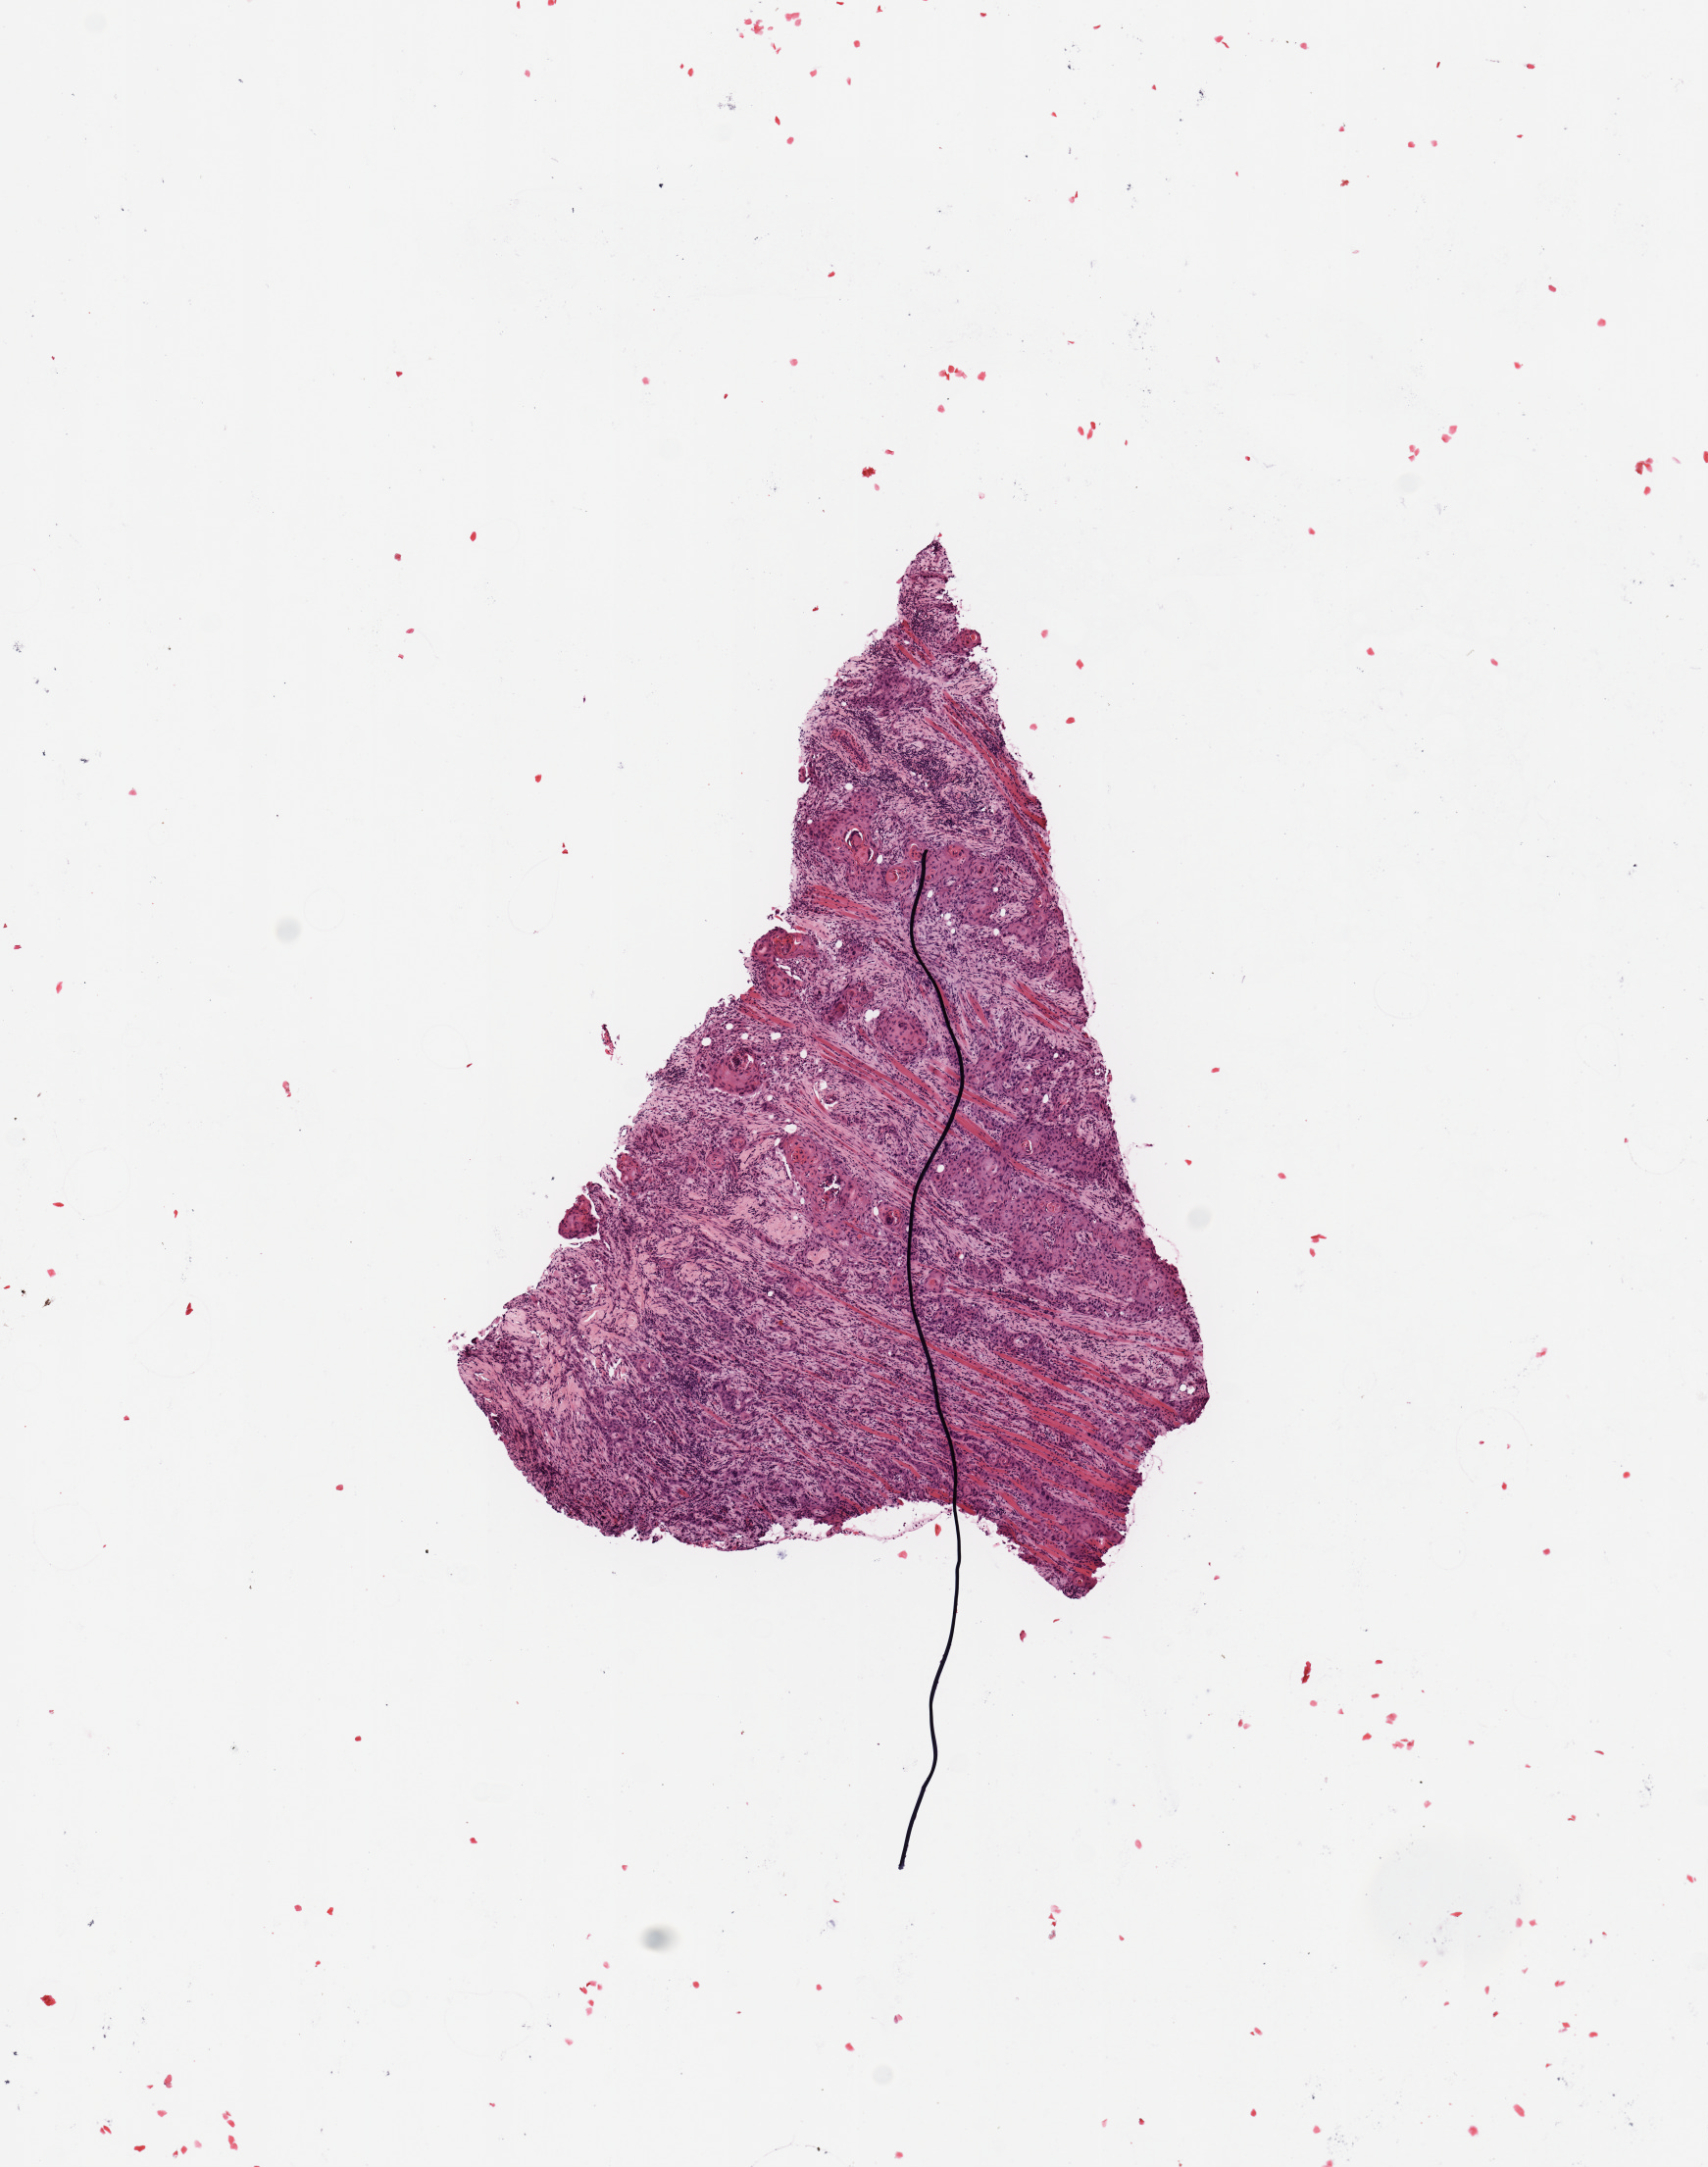
Digitized Hematoxylin and eosin (H&E) stained tissue section (whole slide) — a low-resolution overview of the entire scanned area, about 6.9 x 8.7 mm; tumour tissue sample, sampled site: tongue. Patient: male, age 65 years. Histologic grade: G3 (poorly differentiated). Composition of this section per pathologist review: tumour nuclei 80%, necrosis 0%.
- histologic diagnosis: Squamous cell carcinoma, NOS
- primary tumour site (as recorded): oral cavity
- AJCC pathologic stage: IVA